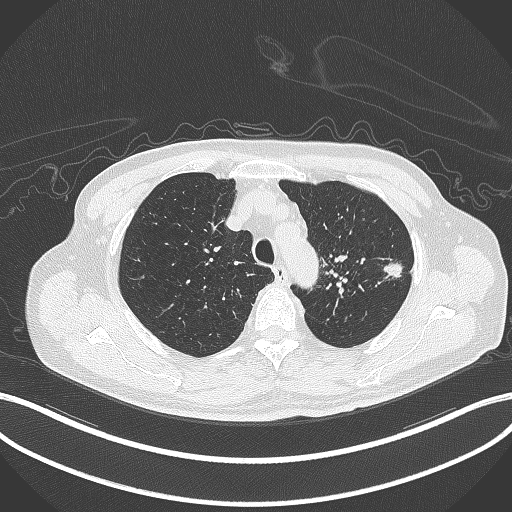
Chest CT, one axial slice. Slice 348 of 417 in the series (ordered by position). Reconstruction kernel B70f. Lung window (W 1500 / L -600 HU). 1 mm slice thickness. 512 × 512 image matrix. Patient: male, 77 years. Case-level facts recorded for this patient, not image findings: clinical TNM (as recorded): T3 N1 M0.
Annotated regions visible in this slice (rectangle marked by the reading radiologist):
- lung tumour (recorded histology: adenocarcinoma): bounding box [x1, y1, x2, y2] px = [382, 258, 404, 280]